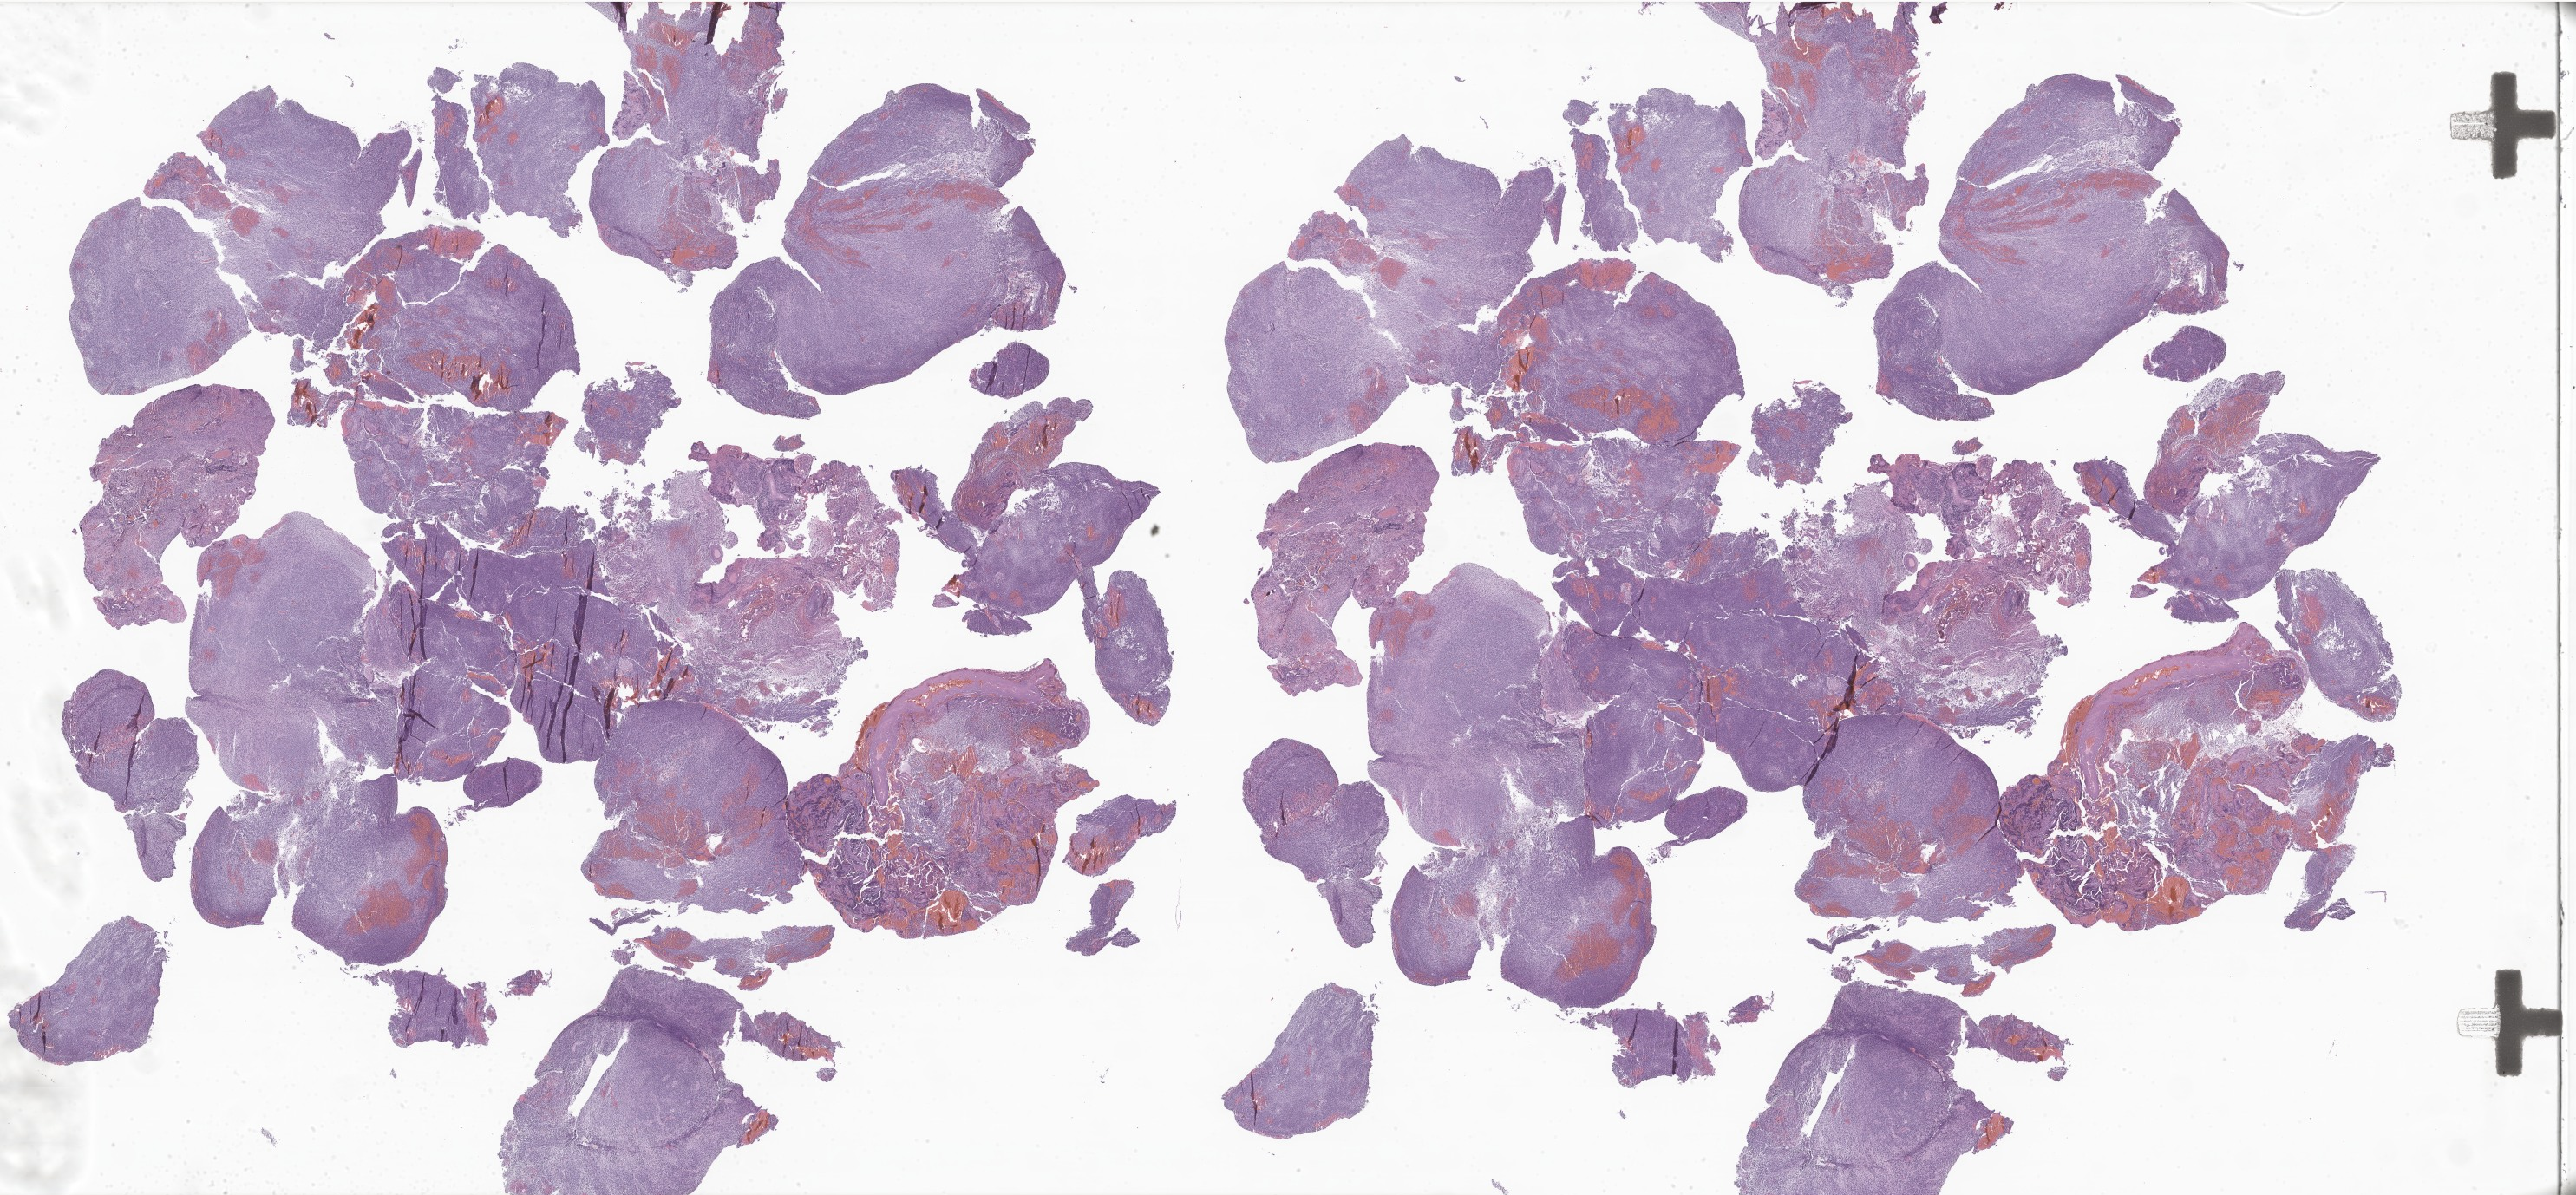
Whole-slide image, H&E stain of tumor tissue from the brain — low-resolution overview of the scanned area, about 50.1 x 23.2 mm, formalin-fixed paraffin-embedded section. Patient: male, age 140 months (11 years 8 months).
• diagnosis (ICD-O-3 morphology term): Medulloblastoma, NOS